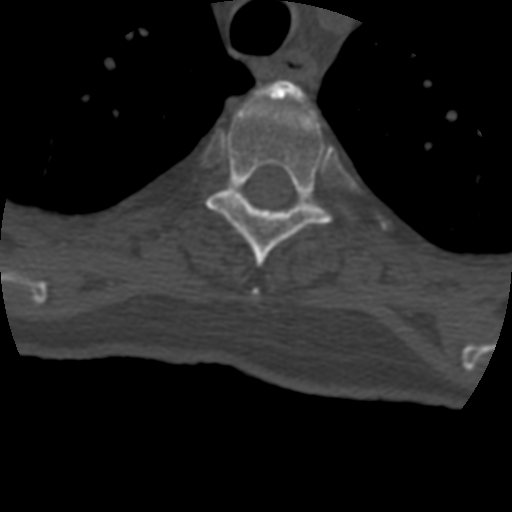
CT including the spine, one axial slice. Position 337 of 399 along the scan axis. 120 kVp. Bone window (W 1800 / L 400 HU). 1.25 mm slice thickness. 512 × 512 image matrix, field of view 160 × 160 mm. Patient age 69 years. From the clinical record (not read from this slice): primary cancer: prostate.
Outlined on this slice (semi-automatic segmentation, software-assisted and operator-edited):
- T3 vertebra: bounding box [x1, y1, x2, y2] px = [256, 82, 302, 98]
- T4 vertebra: [205, 92, 356, 267]